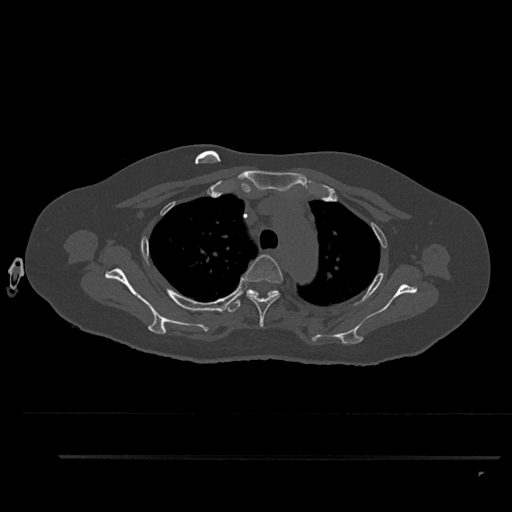
CT including the spine, one axial slice; position 670 of 797 along the scan axis; reconstruction kernel Br40s/3; bone window (W 1800 / L 400 HU); 0.5 mm slice thickness; 512 × 512 image matrix, field of view 408 × 408 mm. Patient: female, 44 years. Case-level facts recorded for this patient, not image findings: primary cancer: renal.
Structures marked on this image (semi-automatically segmented with operator editing):
- T3 vertebra: bounding box [x1, y1, x2, y2] px = [242, 254, 283, 327]
- T4 vertebra: [227, 289, 279, 312]